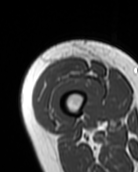
MRI of an extremity soft-tissue mass, one axial slice; position 14 of 99 along the scan axis; MR volume resampled by the dataset authors to the PET/CT grid (not the native acquisition matrix); 3.27 mm slice thickness; 138 × 172 image matrix, field of view 135 × 168 mm. Female patient. Case-level facts recorded for this patient, not image findings: histological type: pleiomorphic undifferentiated sarcoma; grade: high; site of the primary tumour: right quadricep.
Structures marked on this image (expert contour drawn on MRI and transferred to this co-registered scan by the dataset authors):
- gross tumour volume including surrounding oedema: bounding box [x1, y1, x2, y2] px = [35, 59, 86, 112]